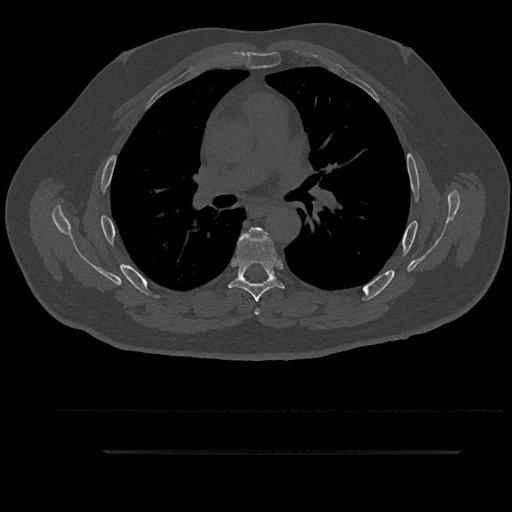
CT including the spine, one axial slice; slice 584 of 797 in the series (ordered by position); reconstruction kernel Br40s/3; 120 kVp; bone window (W 1800 / L 400 HU); 0.5 mm slice thickness; 512 × 512 image matrix, field of view 432 × 432 mm. Male patient, age 63 years. Case-level facts recorded for this patient, not image findings: primary cancer: renal.
Structures marked on this image (semi-automatic segmentation, software-assisted and operator-edited):
- T5 vertebra: bounding box <245,228,267,315> (left, top, right, bottom; pixels)
- T6 vertebra: <227,229,285,302>